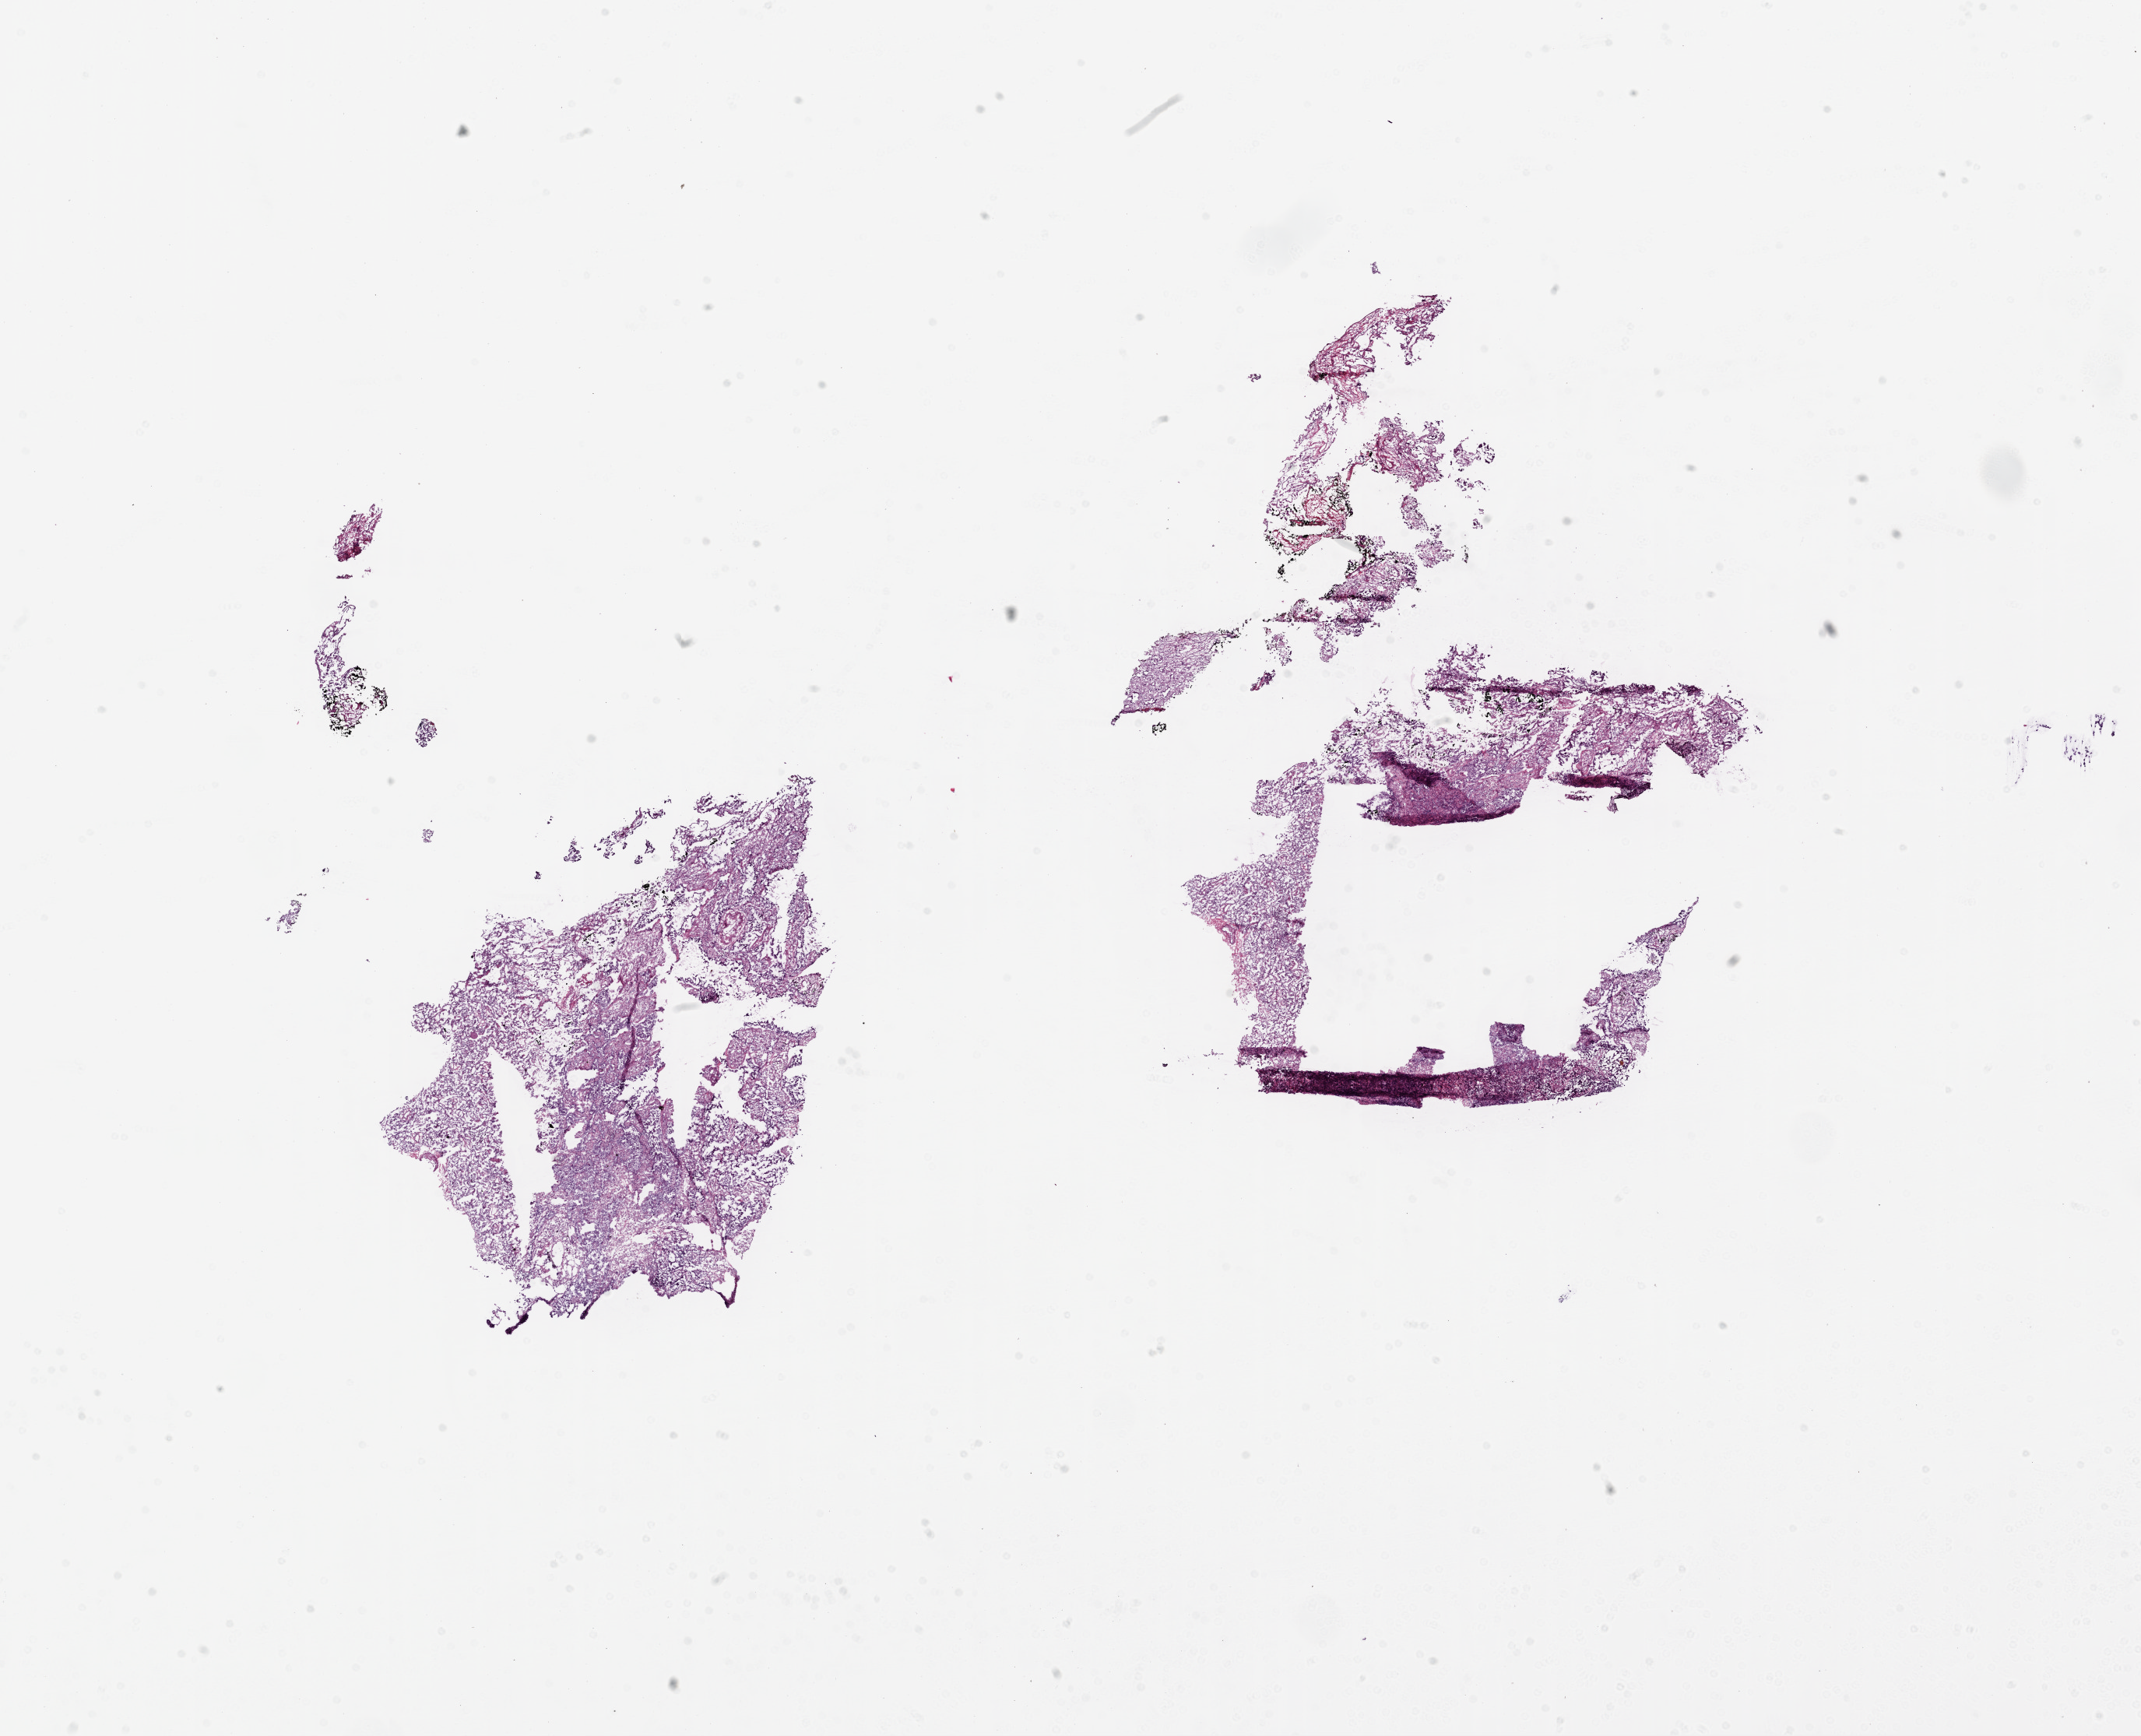
H&E whole-slide image — low-resolution overview of the scanned area, about 22.1 x 17.9 mm. Frozen section from the bottom of the tissue portion. Lung, primary tumour sample. Female, age 67 years at initial diagnosis. Pathologist review of this section (percent, as recorded): tumour cells 85%, tumour nuclei 75%, normal cells 0%, stromal cells 15%, necrosis 0%.
- pathologic diagnosis: Adenocarcinoma, NOS (upper lobe, lung)
- AJCC pathologic stage: IB
- laterality: right